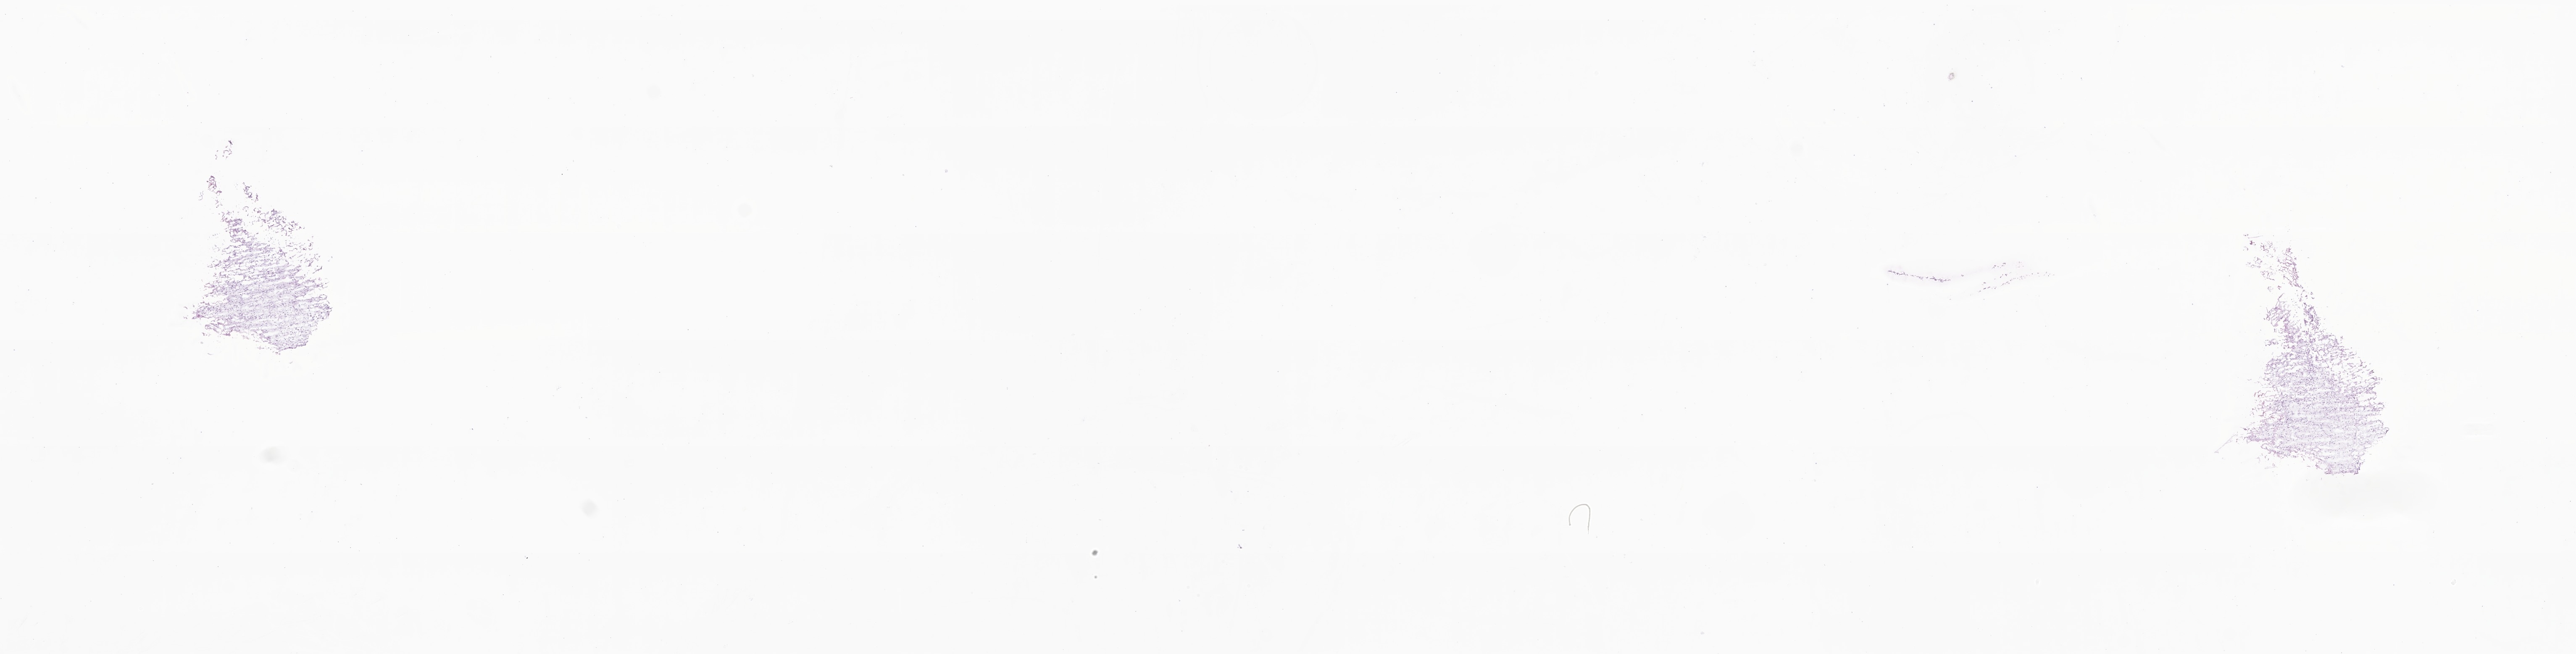
Whole-slide image, haematoxylin and eosin stain of tumor tissue from the brain stem — shown as a low-resolution overview of the whole scanned area (about 25.8 x 6.6 mm). Cryosection (OCT / tissue freezing medium). Patient: male, age 113 months (9 years 5 months).
* diagnosis (ICD-O-3 morphology term): Glioma, malignant